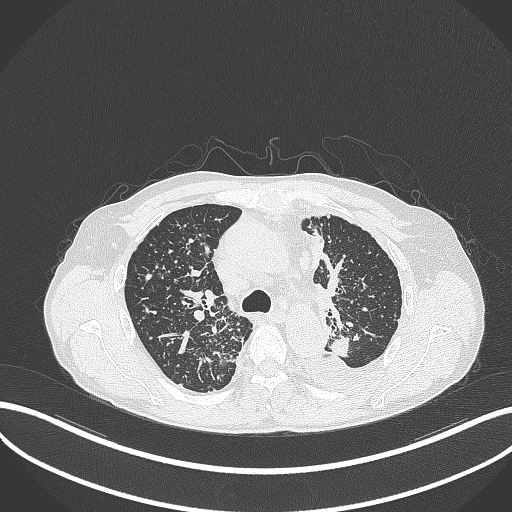
Chest CT, one axial slice; slice 250 of 325 in the series (ordered by position); reconstruction kernel B70f; lung window (W 1500 / L -600 HU); 1 mm slice thickness; 512 × 512 image matrix, field of view 400 × 400 mm. Male patient, age 58 years. From the clinical record (not read from this slice): clinical TNM (as recorded): T1c N3 M1.
Outlined on this slice (bounding box drawn by a radiologist):
- lung tumour (recorded histology: adenocarcinoma): bounding box <329,334,350,358> (left, top, right, bottom; pixels)